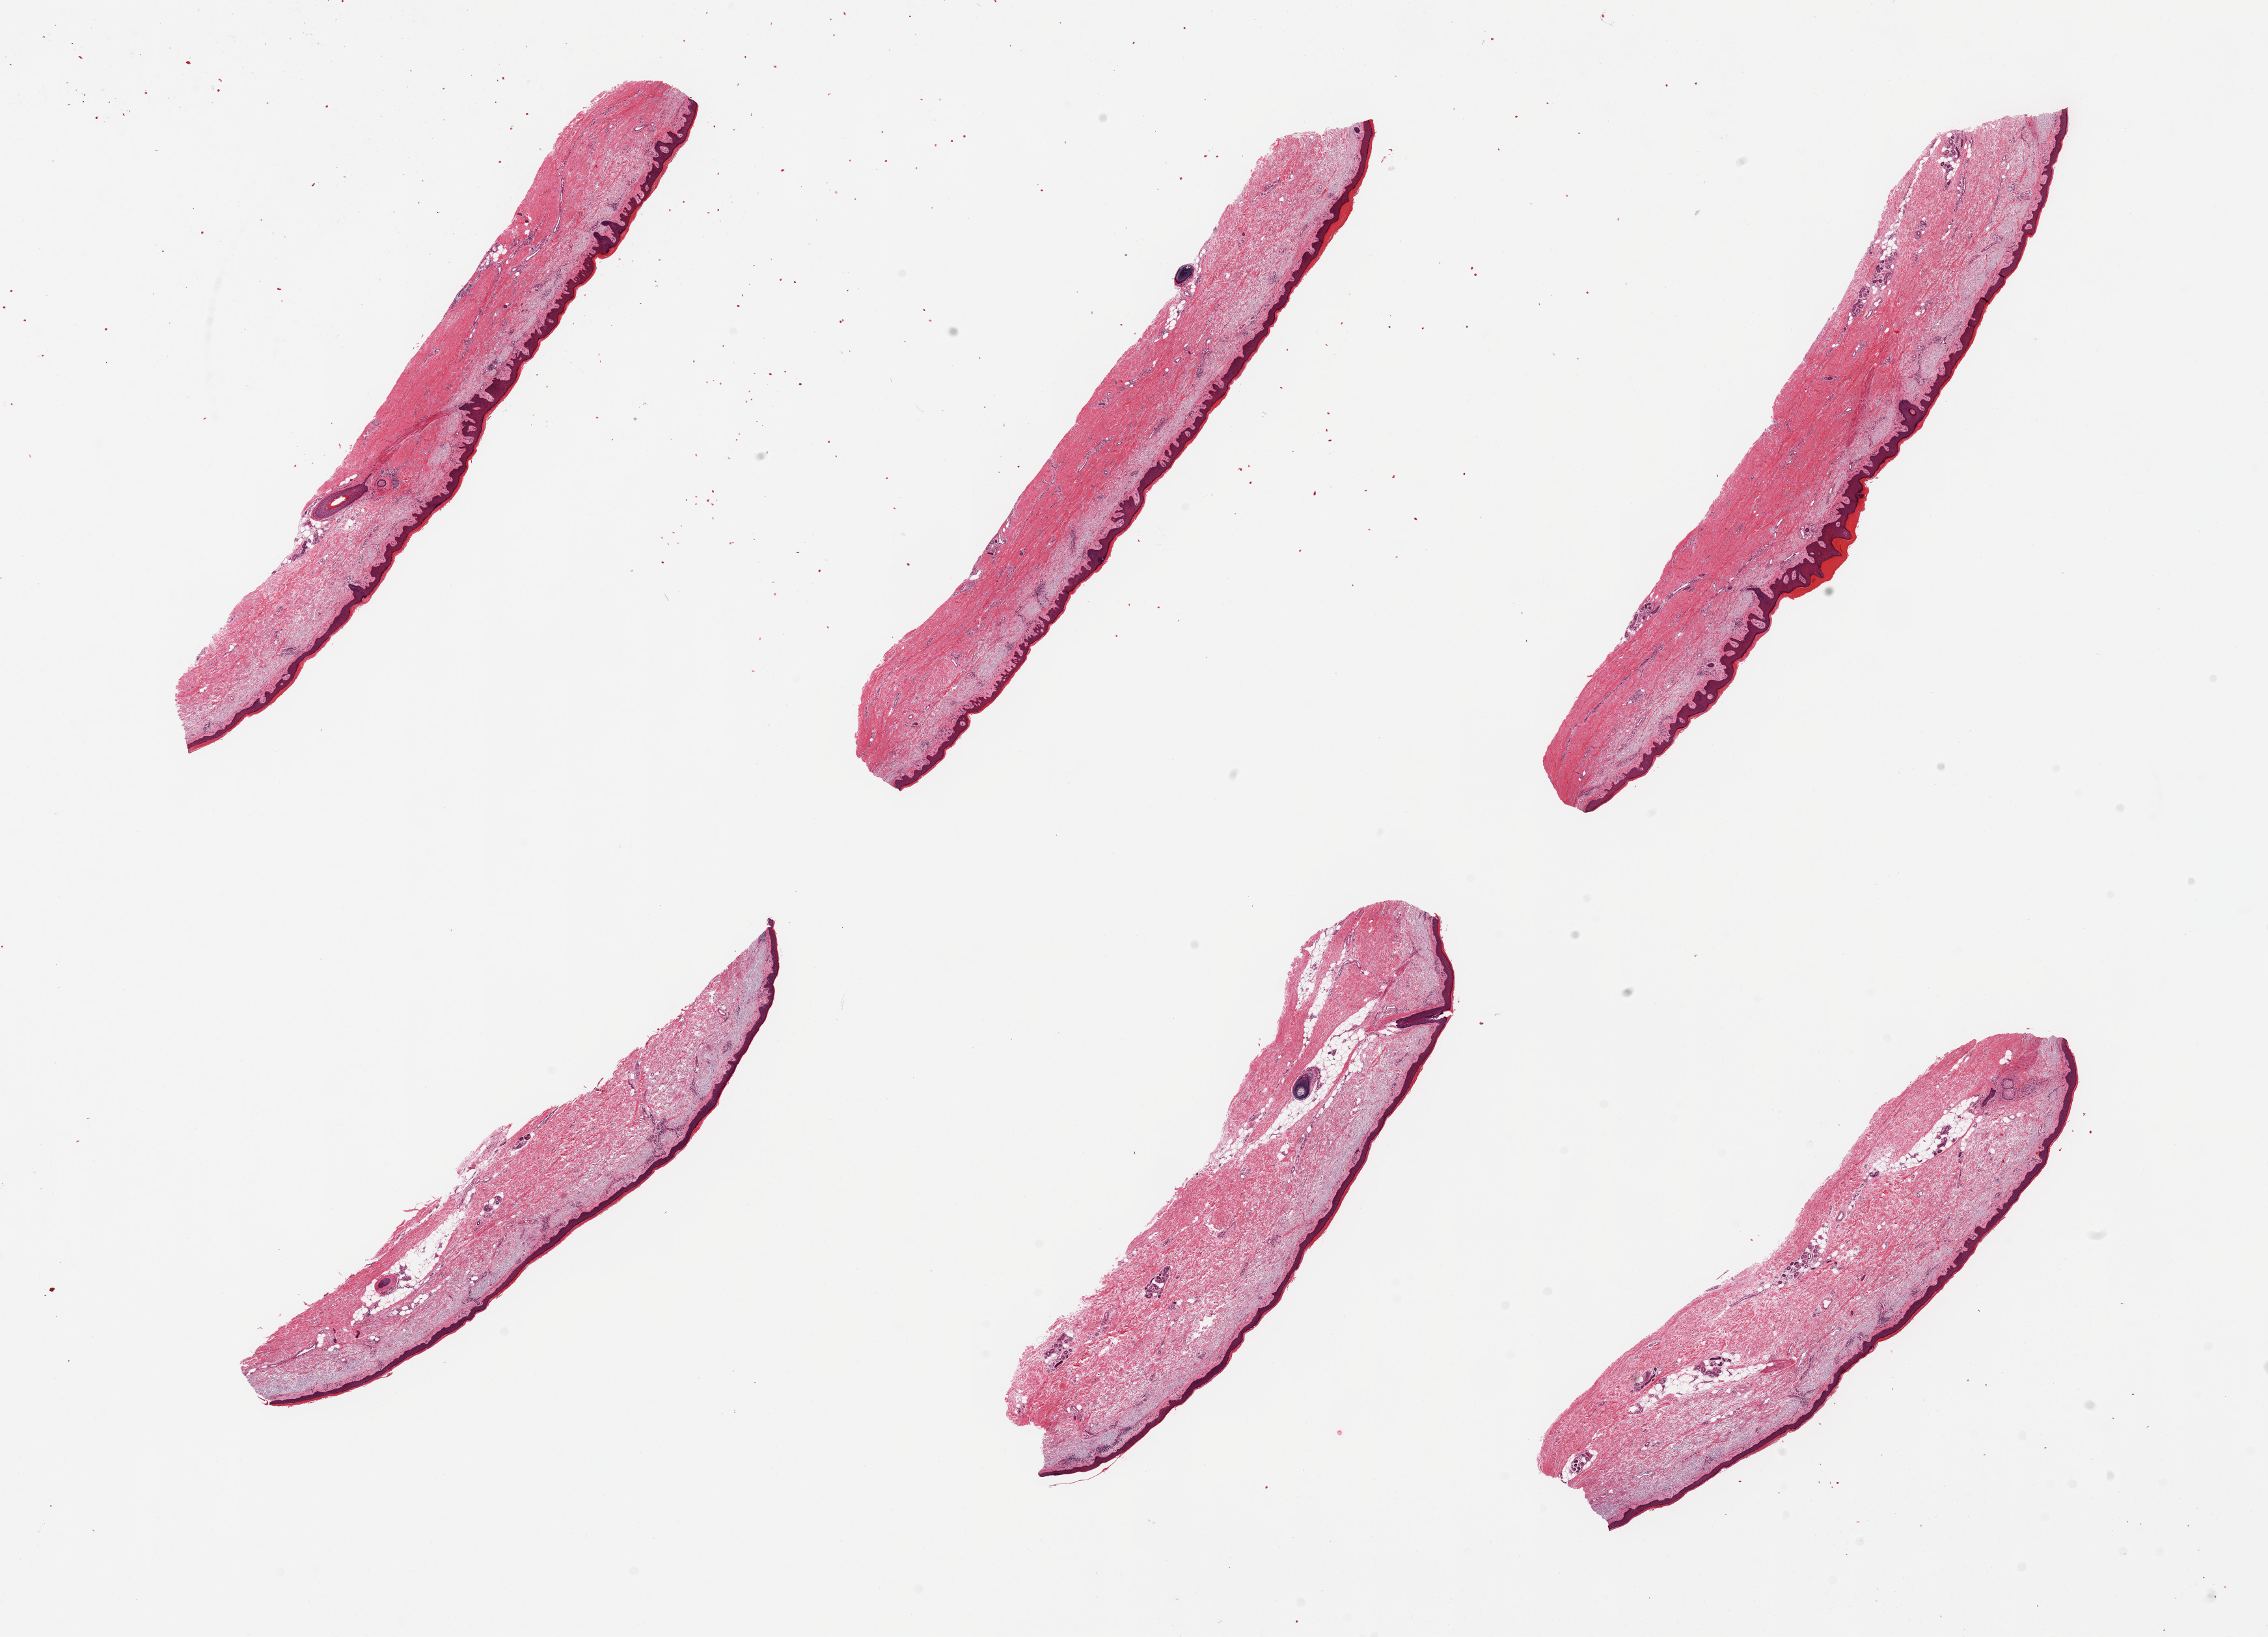
Whole-slide image, hematoxylin and eosin (H&E) stain — a low-resolution overview of the entire scanned area, about 27.6 x 19.9 mm (acquisition: 20x scan); PAXgene-fixed, paraffin-embedded tissue; sampled site (target tissue): skin of lower leg; tissue donor sample.
- reviewer comment on this tissue sample: 6 pieces; solar elastosis, epidermis measures about 67 microns